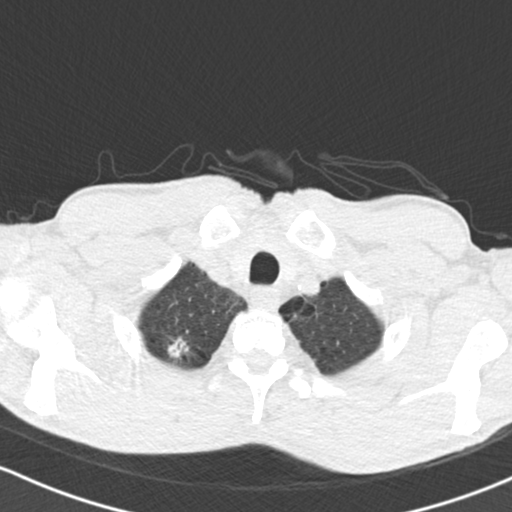
Low-dose screening chest CT, one axial slice; position 127 of 150 along the scan axis; 120 kVp; lung window (W 1500 / L -600 HU); 2 mm slice thickness; 512 × 512 image matrix, field of view 312 × 312 mm.
Outlined on this slice (expert manual segmentation):
- lesion 1 (tumor, upper lobe of right lung): box from (x=168, y=338) to (x=189, y=358) px